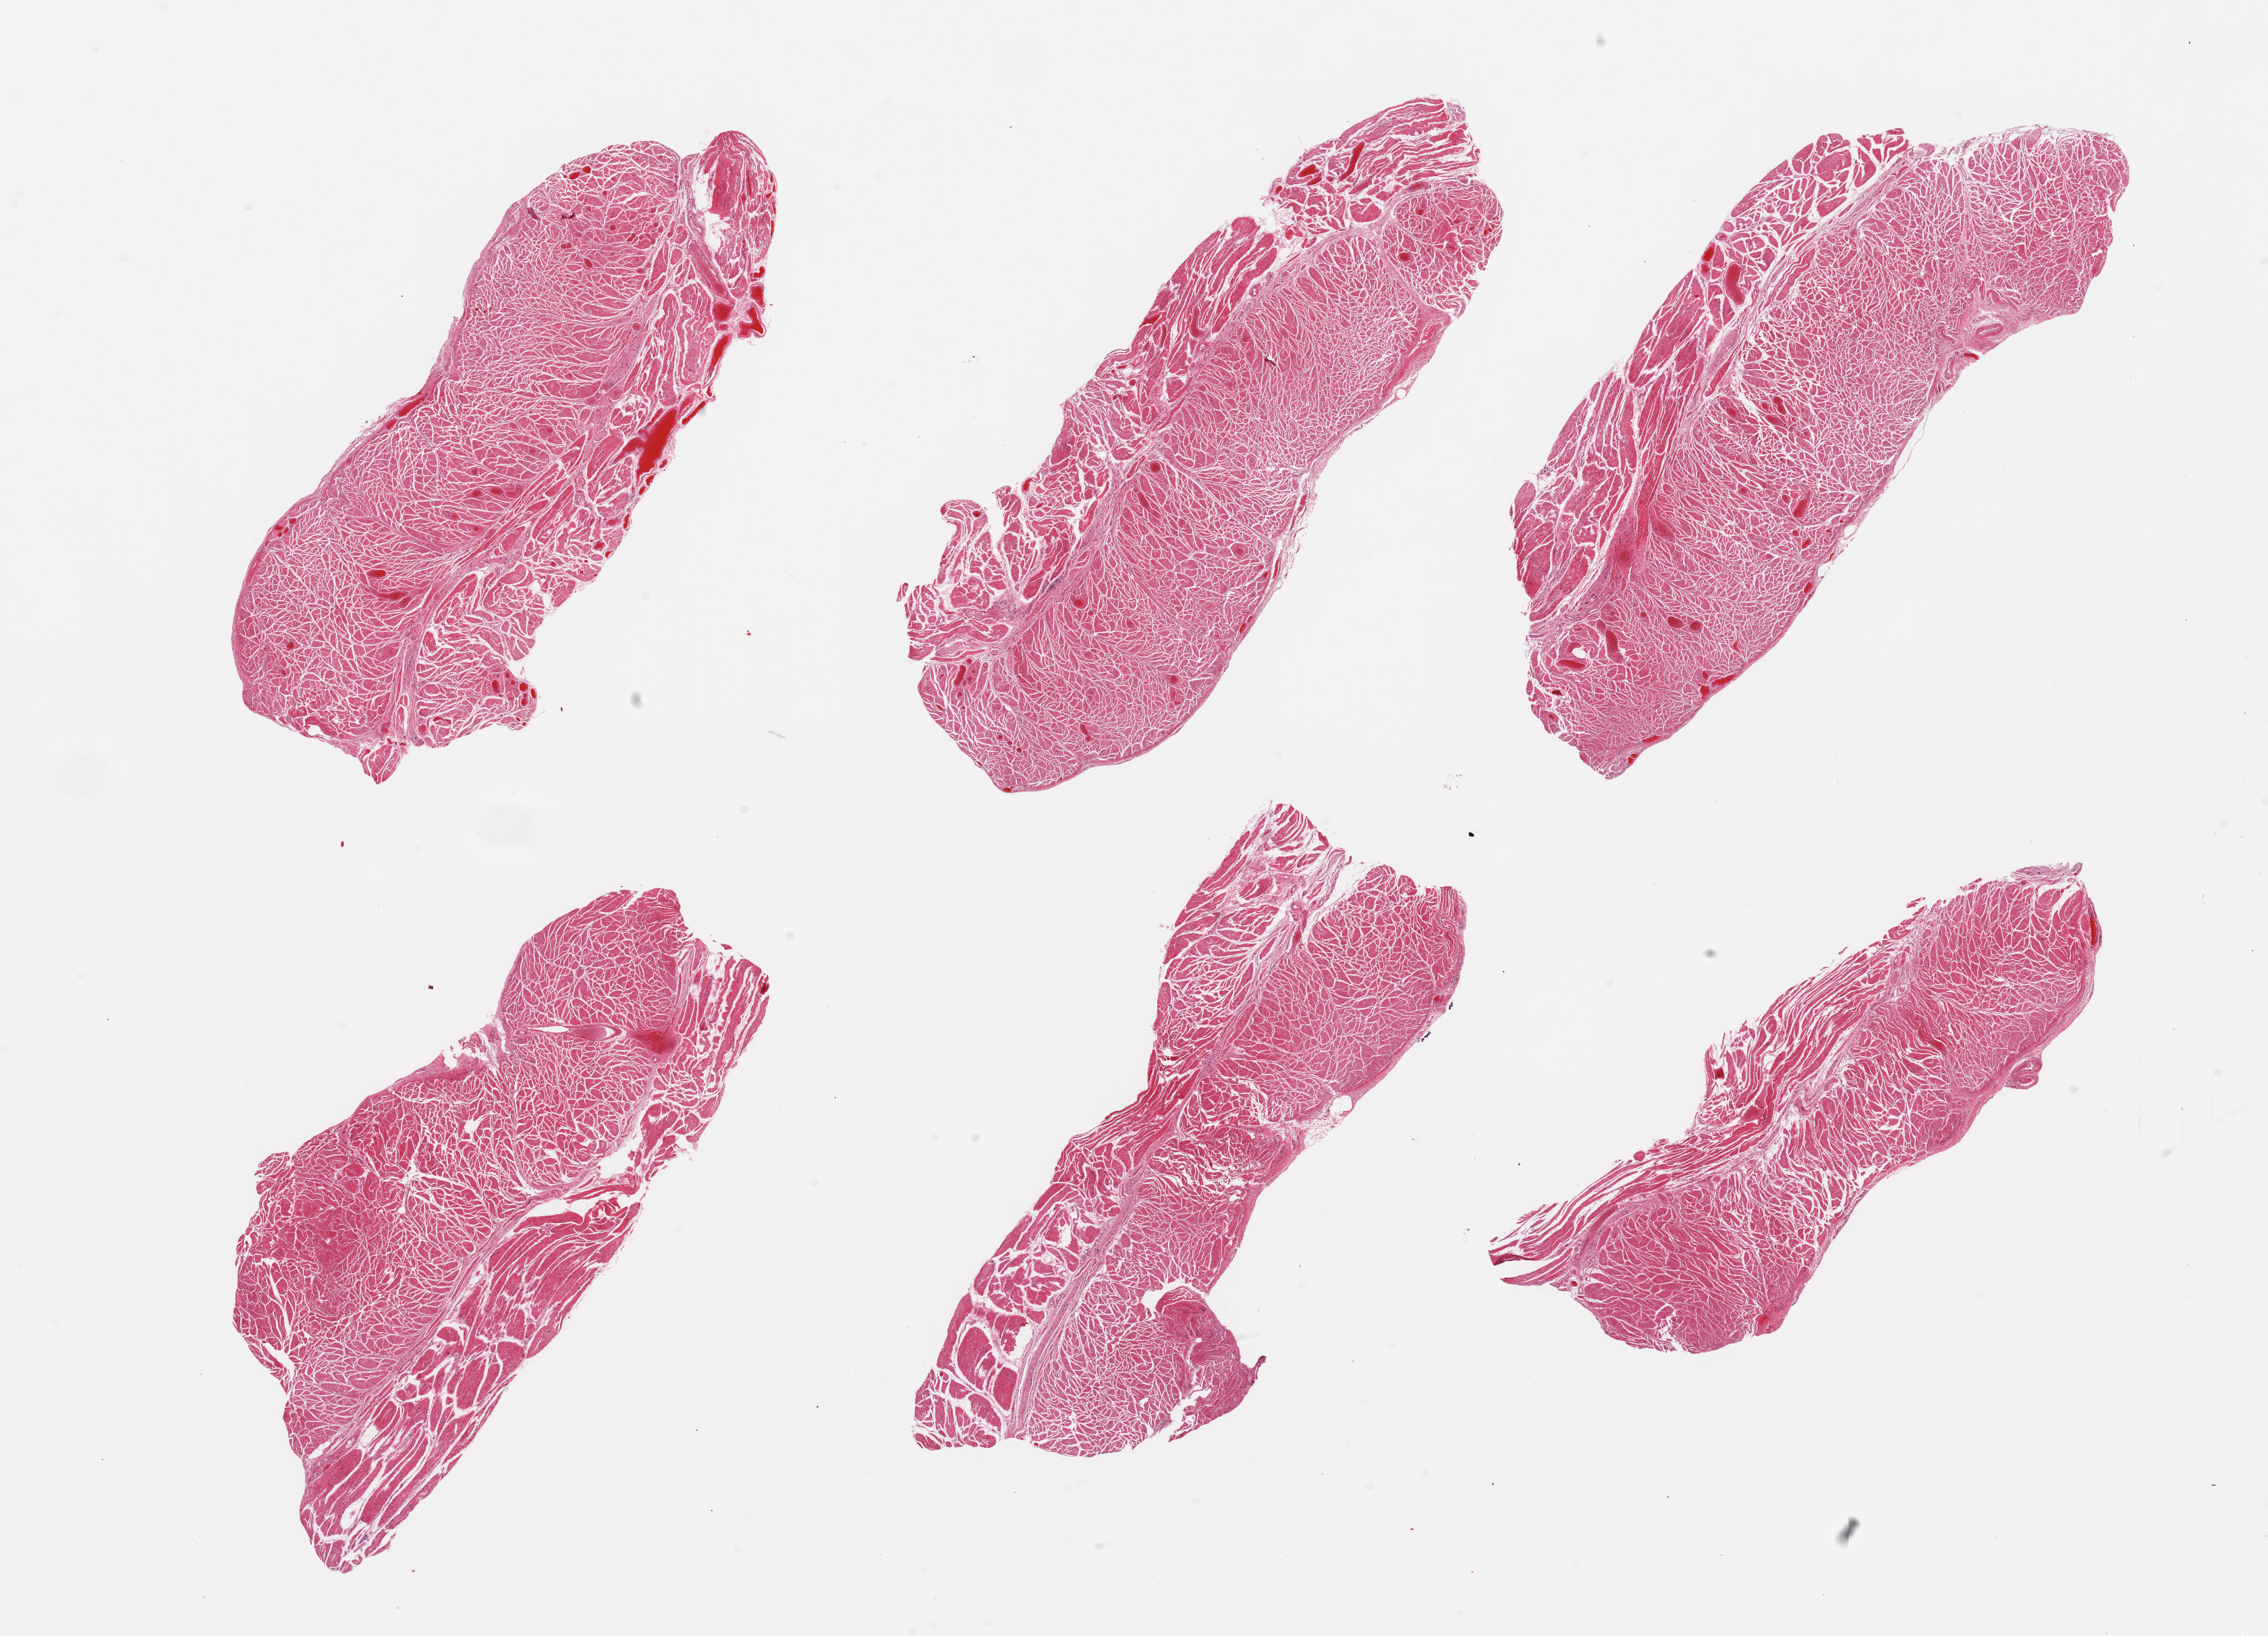
Whole-slide image, haematoxylin and eosin stain, low-resolution overview of the scanned area, about 26.6 x 19.2 mm; PAXgene-fixed, paraffin-embedded tissue; sampled site (target tissue): gastroesophageal junction; tissue donor sample. Donor: male.
Review note (as recorded): 6 pieces, confirmed target muscularis.